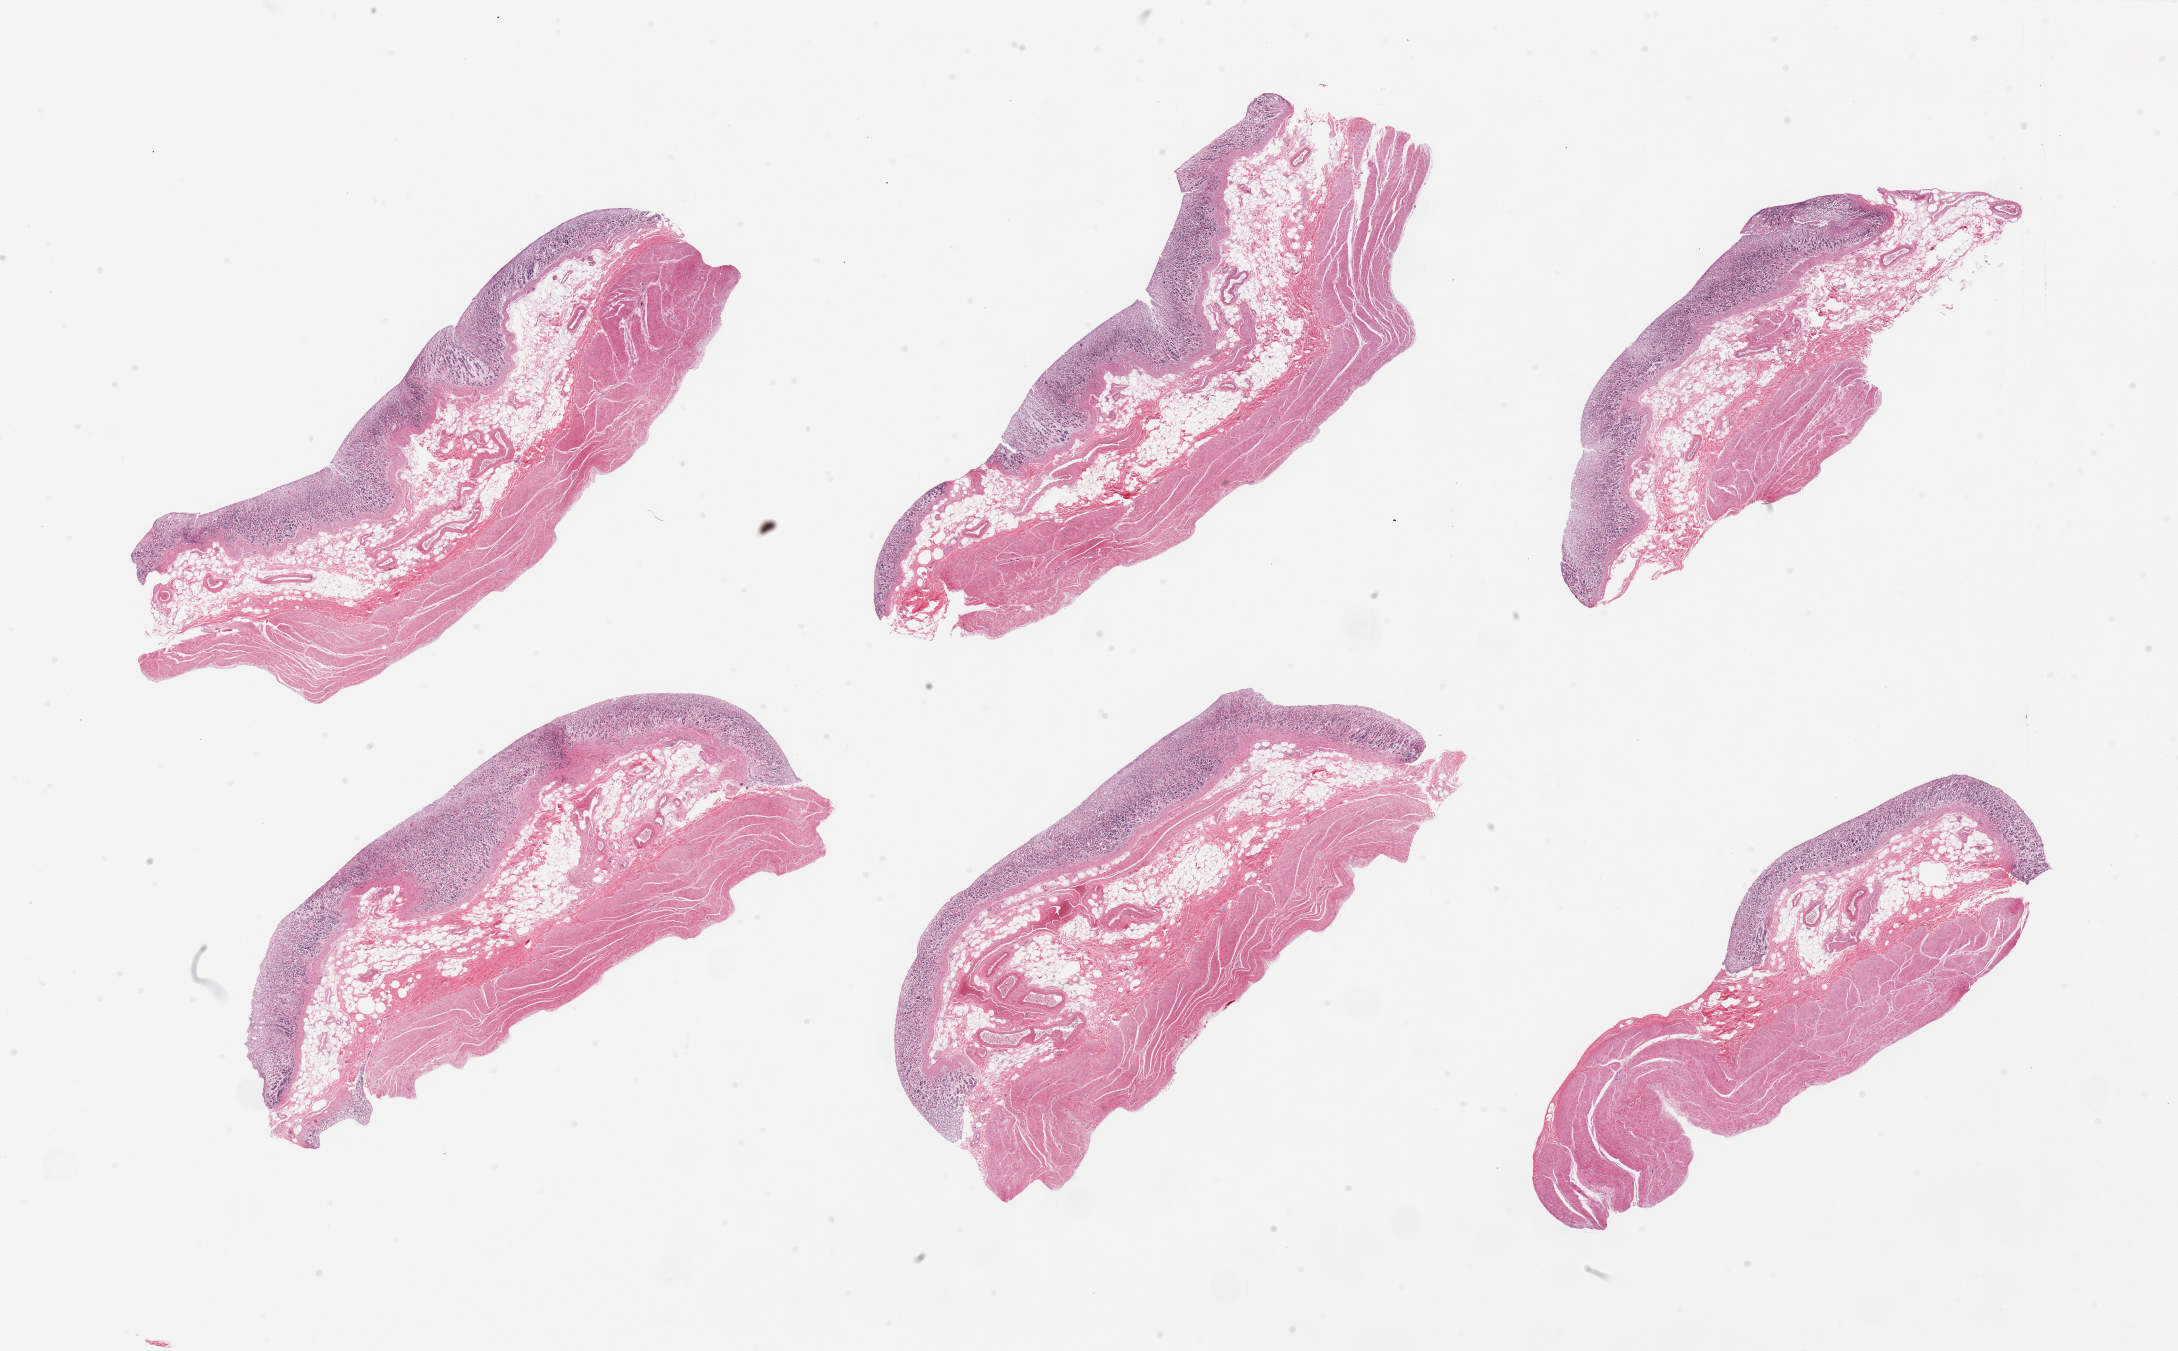
Hematoxylin and eosin (H&E) whole-slide image, whole scanned area (about 34.5 x 21.4 mm) shown as a low-resolution overview; PAXgene-fixed, paraffin-embedded tissue; target tissue: stomach; donor tissue sample. Donor sex: male.
Pathologist's review note for this sample: 6 pieces, mucosa is ~0.7mm, ~25% thickness, advanced autolysis.